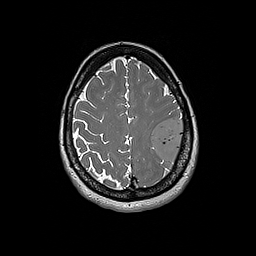
Brain MRI from a brain-tumour surgery series, one axial slice; 1 mm slice thickness; 256 × 256 image matrix, field of view 250 × 250 mm. From the clinical record (not read from this slice): histopathology: Glioblastoma; WHO grade: 4; IDH mutation: no; tumour location: Left Frontal.
Structures marked on this image (manually delineated by an expert):
- tumour: bounding box [x1, y1, x2, y2] px = [152, 115, 184, 165]